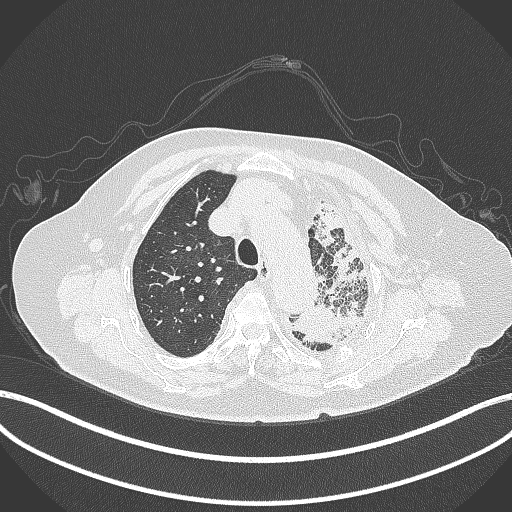
Chest CT, one axial slice. Slice 303 of 399 in the series (ordered by position). Lung window (W 1500 / L -600 HU). 1 mm slice thickness. 512 × 512 image matrix, field of view 400 × 400 mm. Female patient, age 75 years. From the clinical record (not read from this slice): clinical TNM (as recorded): T3 N3 M1.
Annotated regions visible in this slice (bounding box drawn by a radiologist):
- lung tumour (recorded histology: adenocarcinoma): bounding box <283,300,366,350> (left, top, right, bottom; pixels)